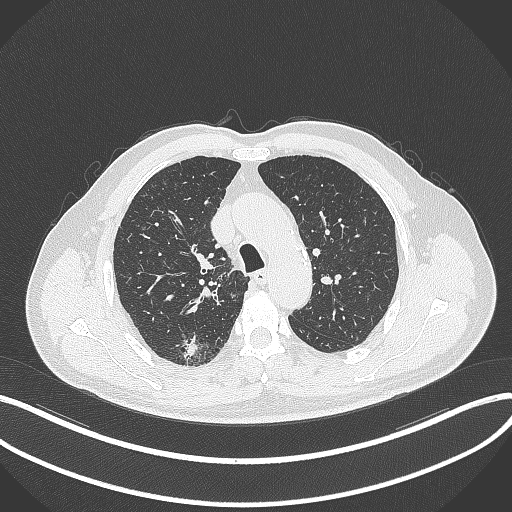
Chest CT, one axial slice; slice 271 of 359 in the series (ordered by position); lung window (W 1500 / L -600 HU); 512 × 512 image matrix, field of view 400 × 400 mm. Male patient, age 69 years. Case-level facts recorded for this patient, not image findings: clinical TNM (as recorded): T1b N0 M0; histopathological grade: G2-3.
Structures marked on this image (rectangle marked by the reading radiologist):
- lung tumour (recorded histology: adenocarcinoma): box from (x=179, y=336) to (x=201, y=360) px